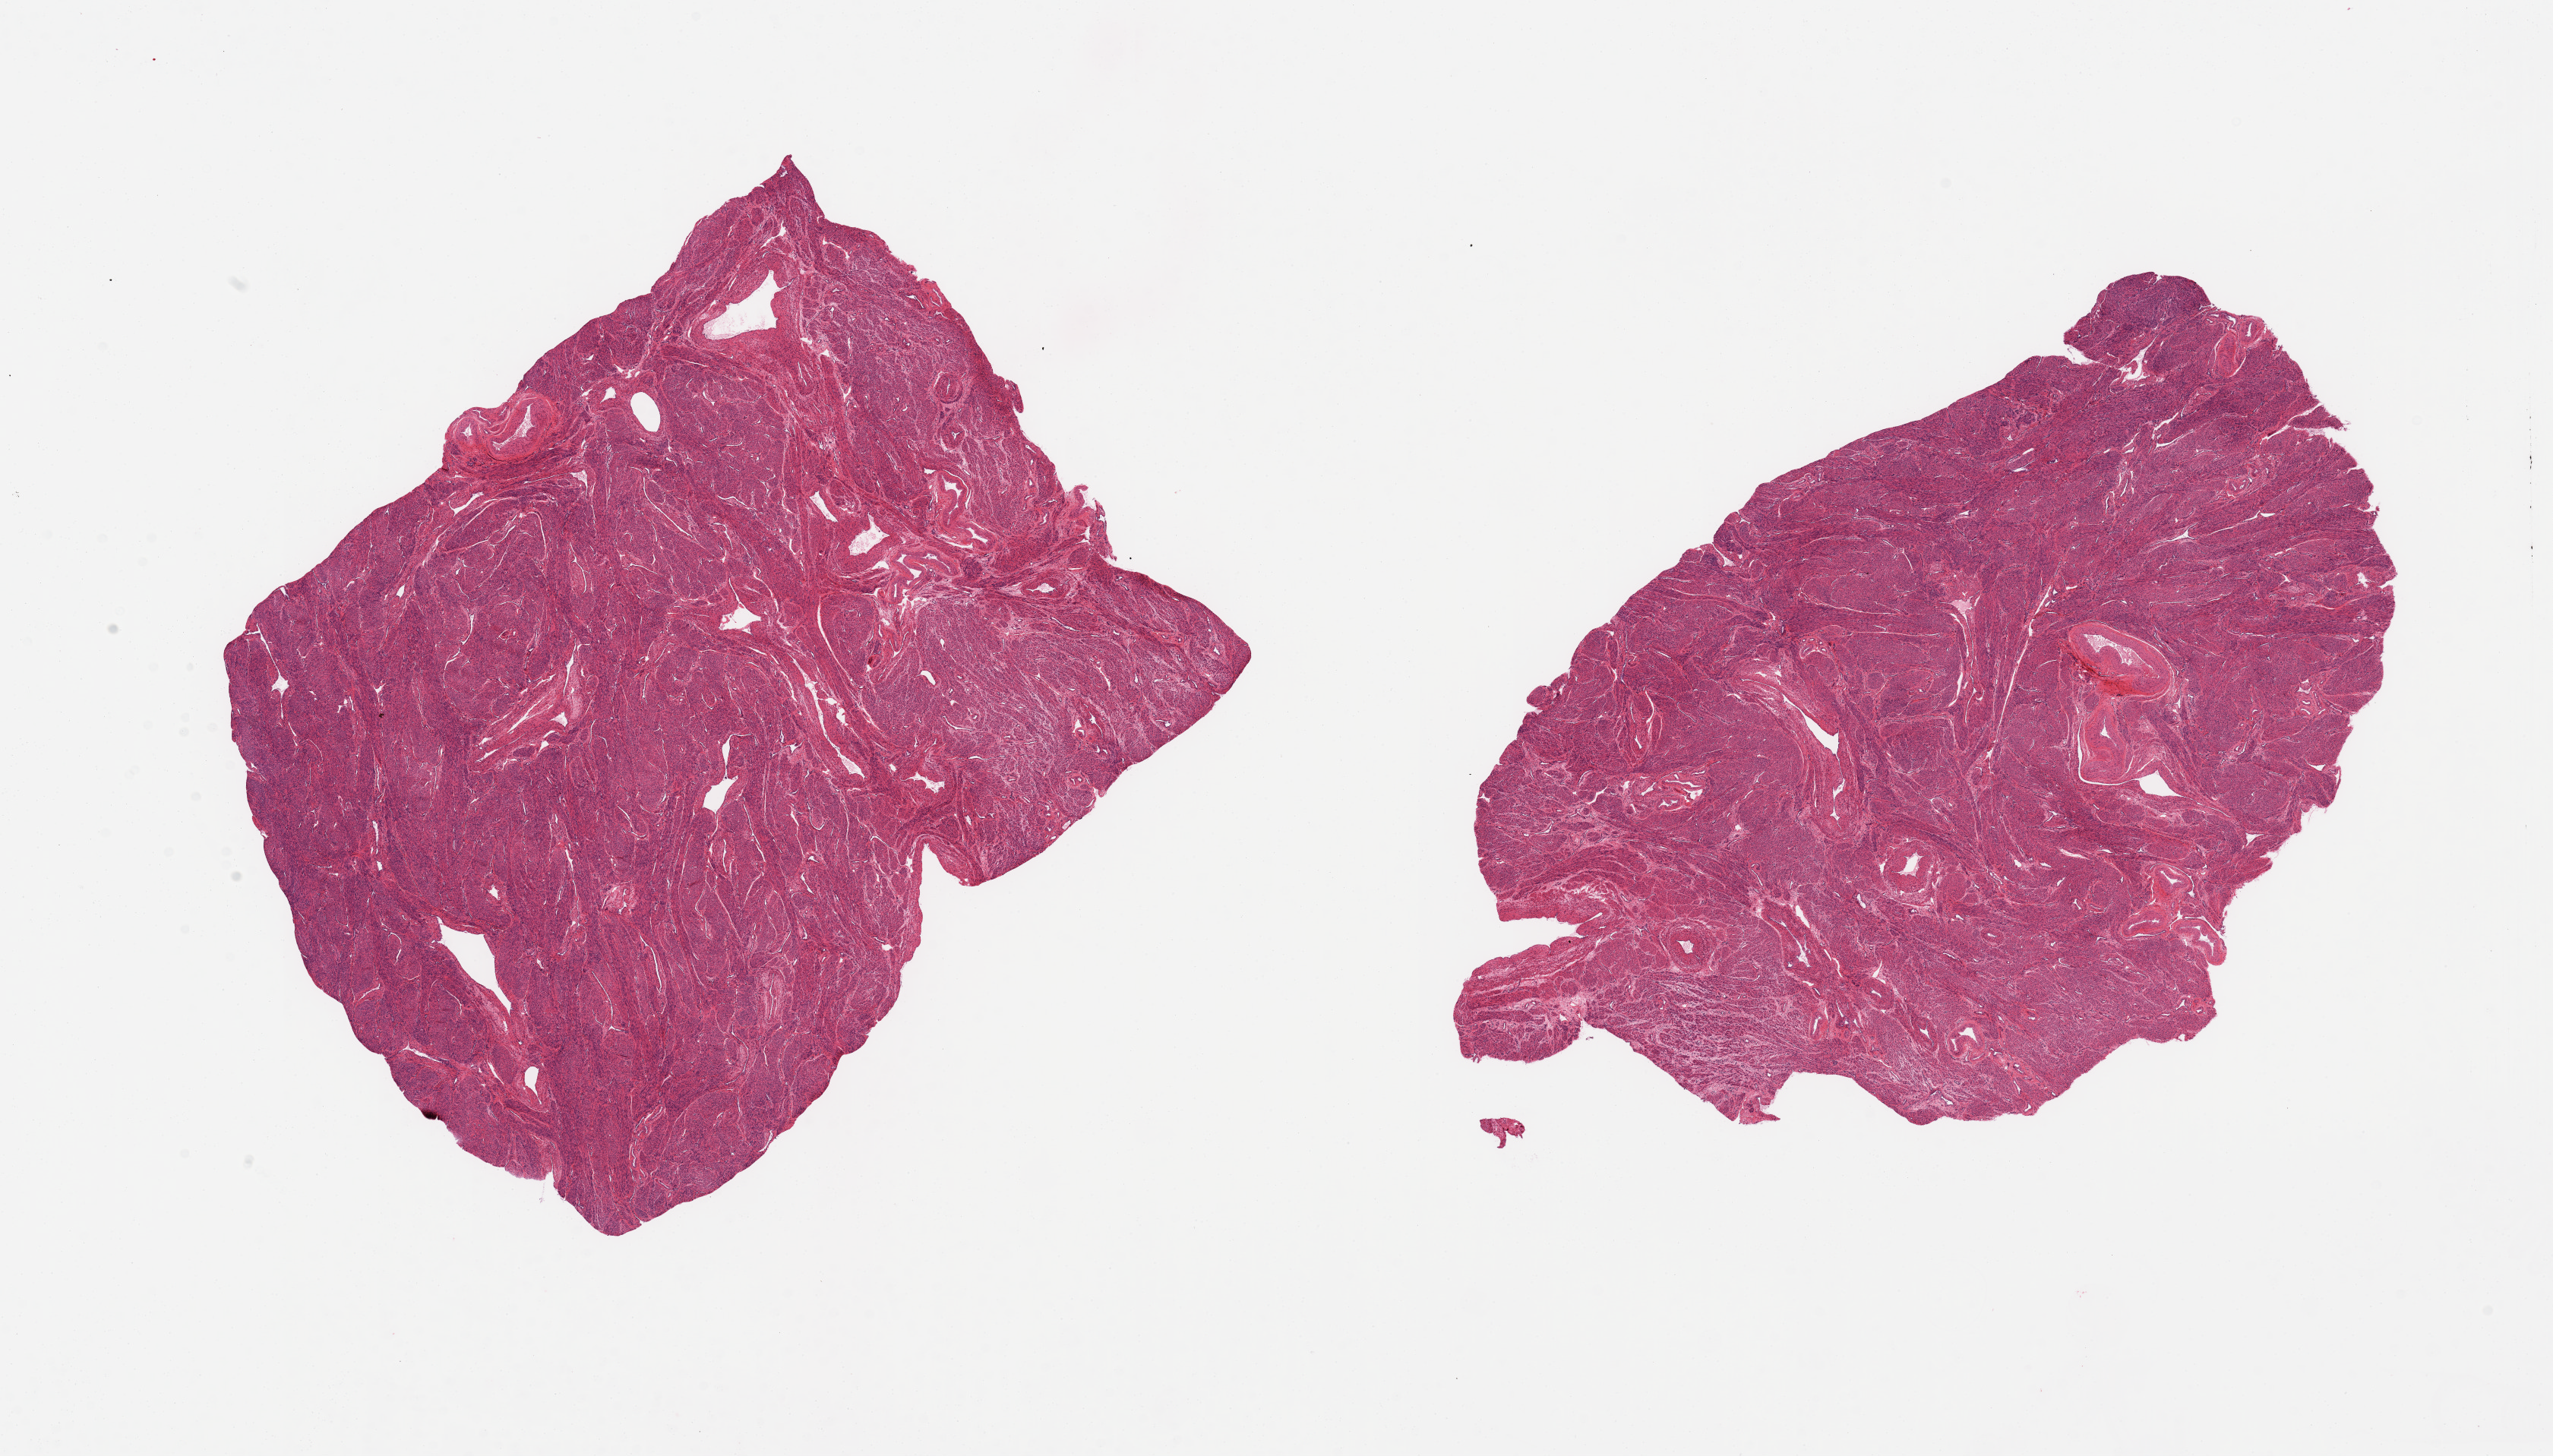
Hematoxylin and eosin (H&E) whole-slide image — whole scanned area (about 26.6 x 15.2 mm) shown as a low-resolution overview, PAXgene-fixed, paraffin-embedded tissue, target tissue: uterus, tissue donor sample. Donor: female.
Review note (as recorded): 2 pieces, all myometrium; no endometrial glands/stroma.